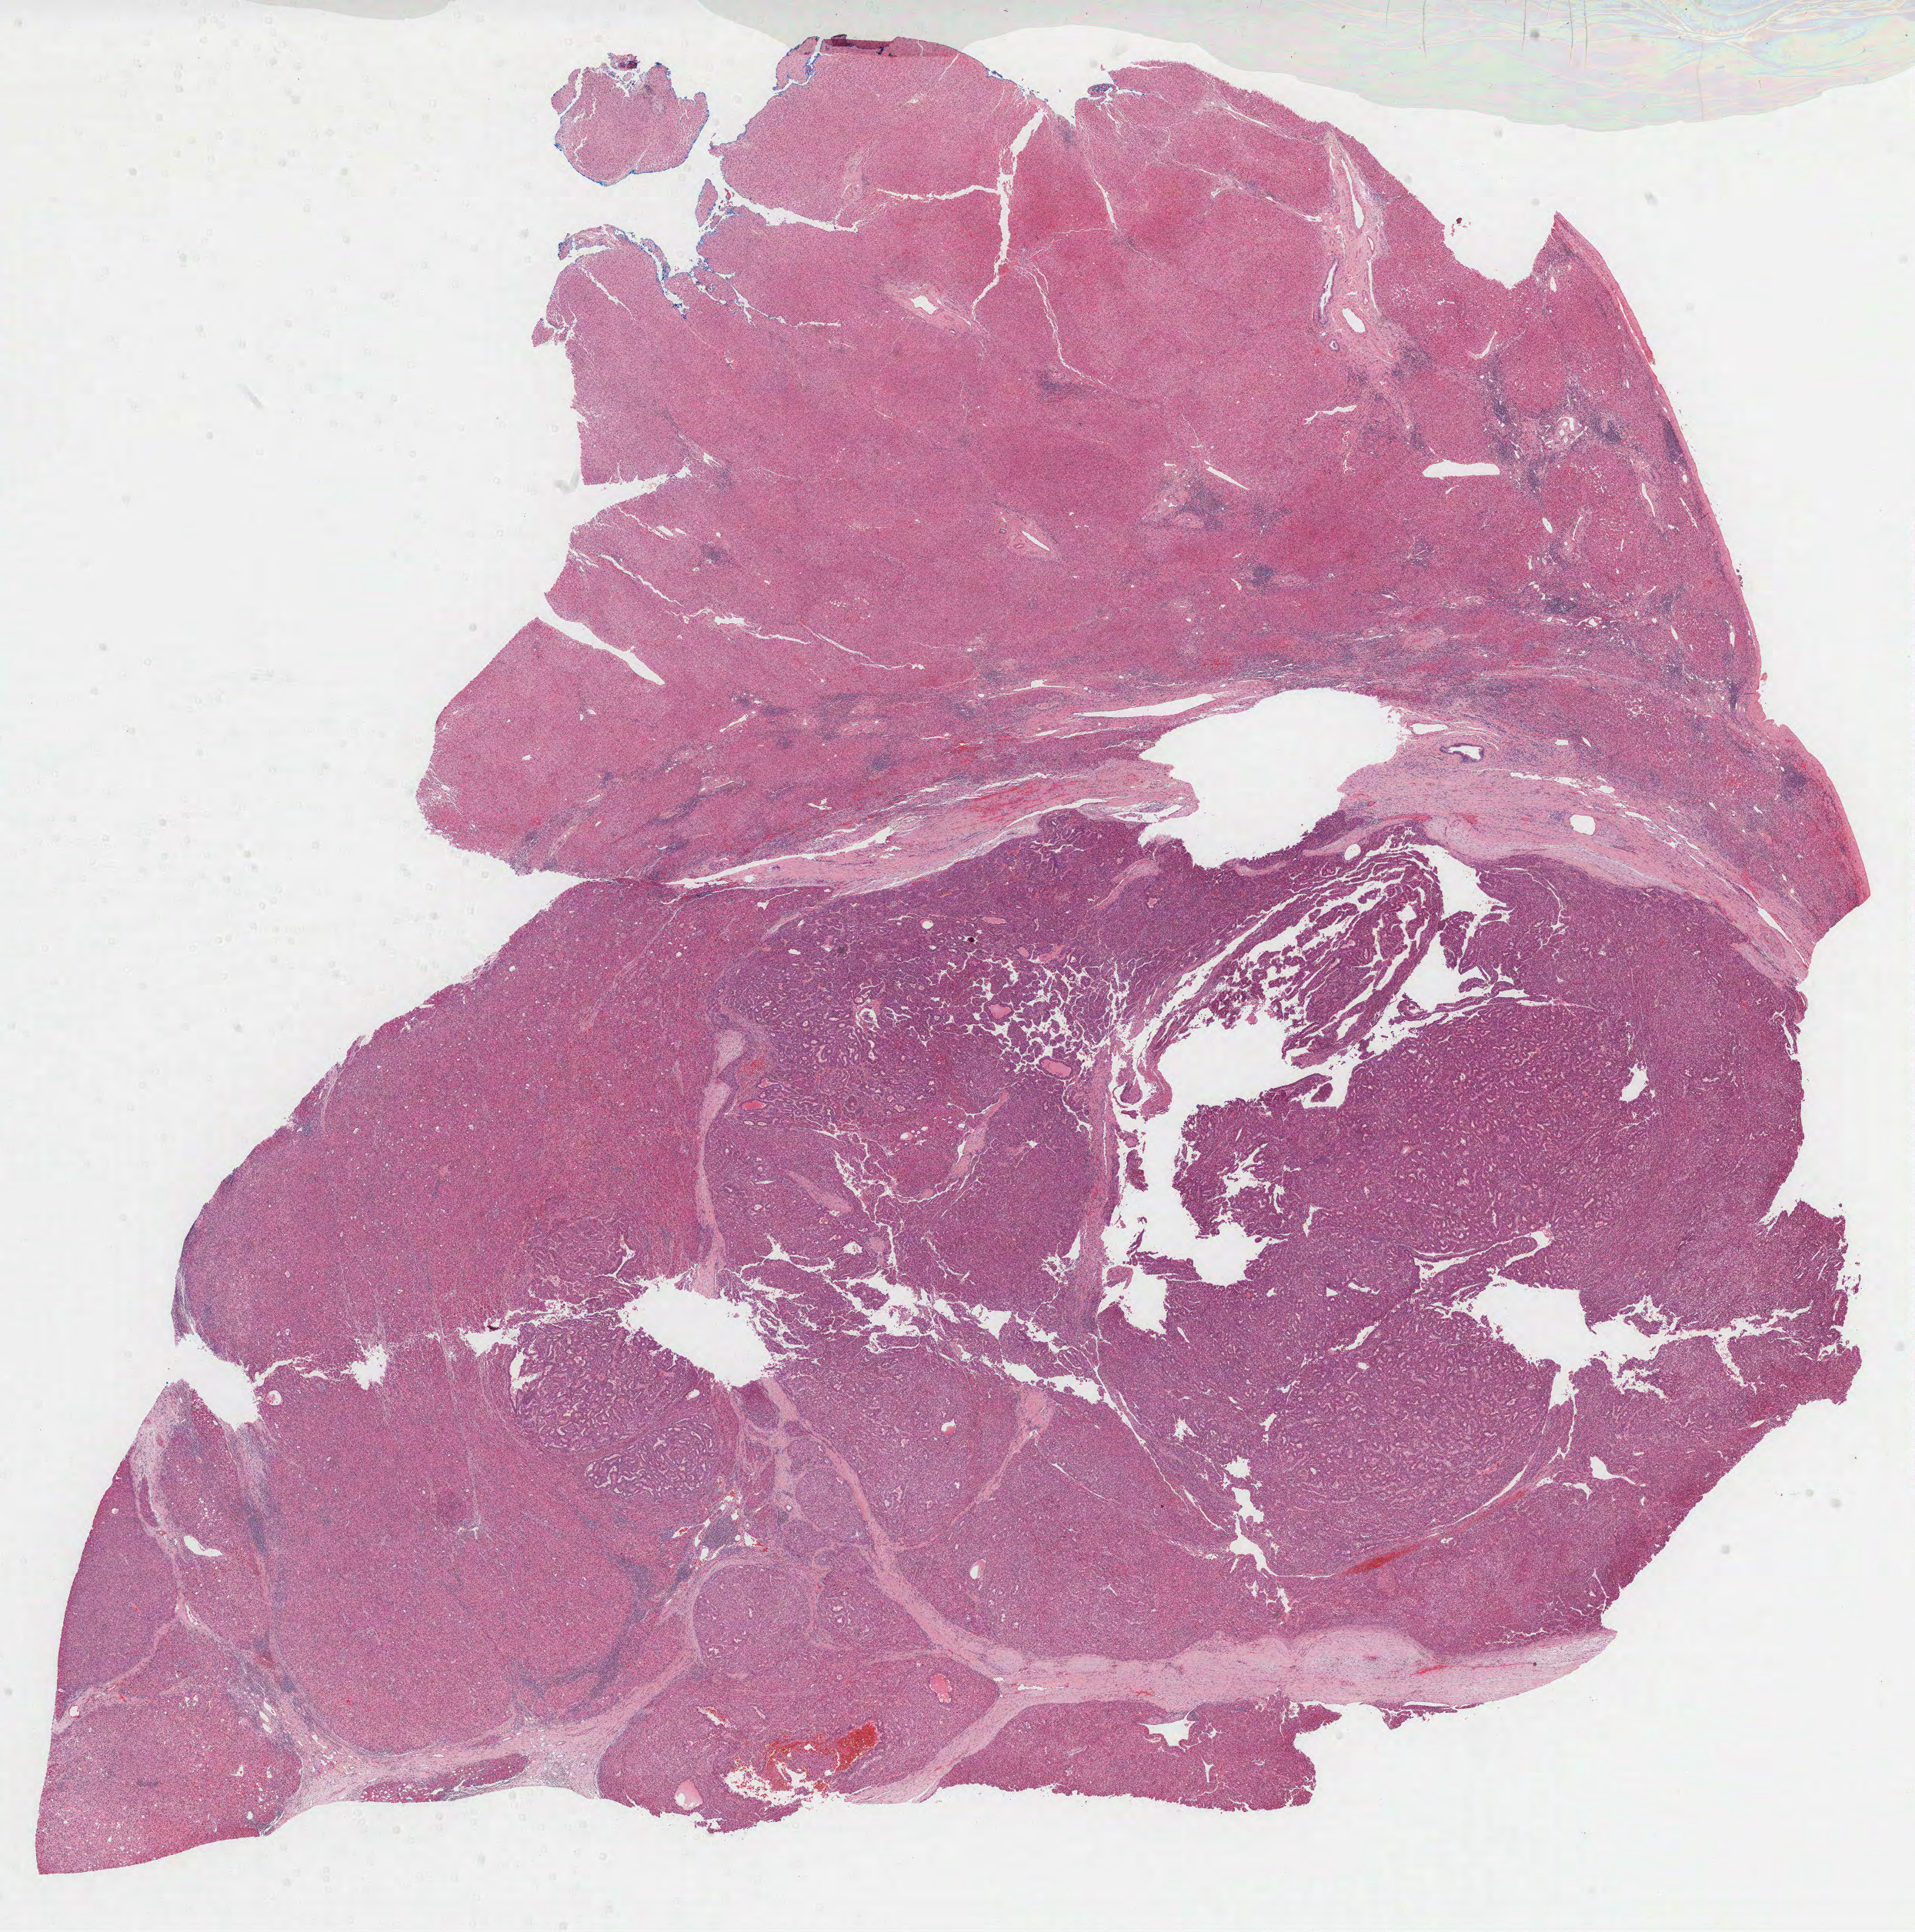
H&E whole-slide image, a low-resolution overview of the entire scanned area, about 20.1 x 20.3 mm (acquisition: 40x scan). Formalin-fixed paraffin-embedded (FFPE) diagnostic section. Sample: primary tumour, liver. Patient: male, age at initial diagnosis 58 years. Histologic grade: G2 (moderately differentiated).
AJCC pathologic stage: I (7th edition). Pathologic diagnosis: Hepatocellular carcinoma, NOS.